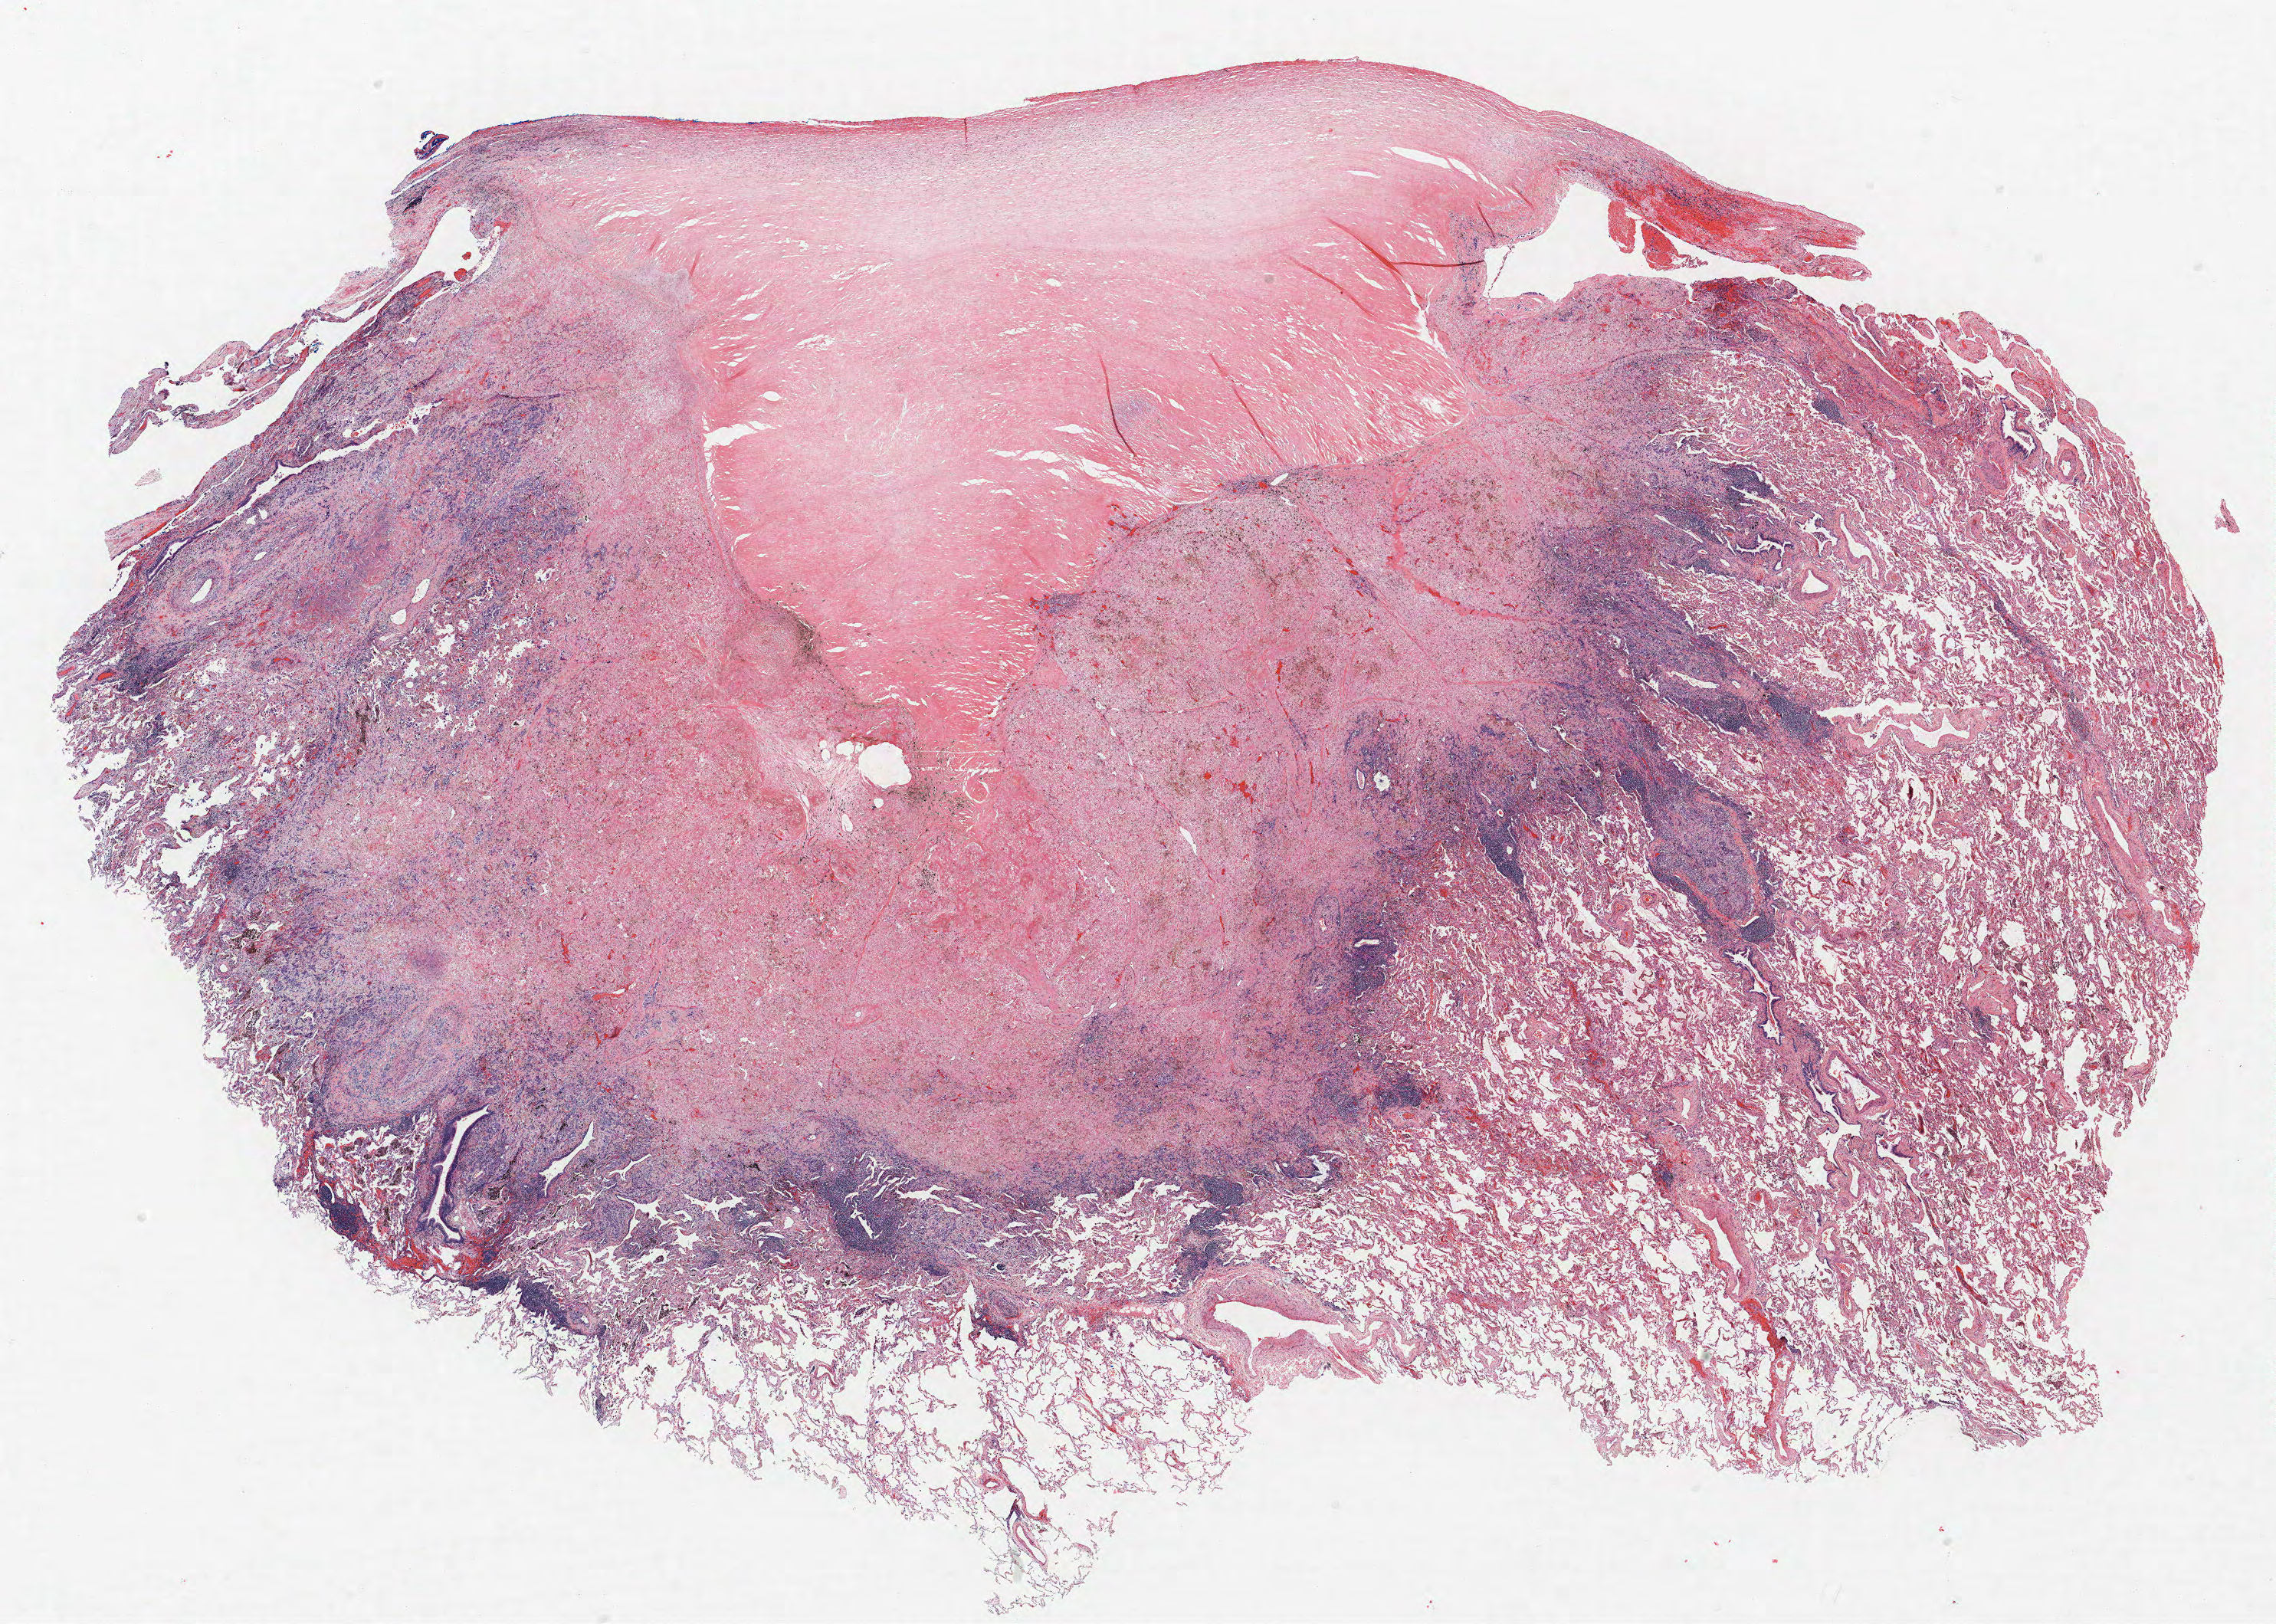
Whole-slide histology image, H&E — shown as a low-resolution overview of the whole scanned area (about 23.8 x 17.0 mm). Formalin-fixed paraffin-embedded (FFPE) section. Lung tissue. Female, age 61 at enrolment. Grade: poorly differentiated (G3).
Primary tumour location (clinical record): left upper lobe. Participant's lung-cancer diagnosis: Adenocarcinoma, NOS (ICD-O-3 8140/3). Stage (AJCC 6th edition): IB. Tumour size (pathology): 17 mm.